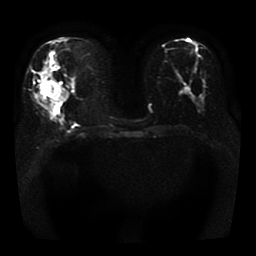
Breast MRI, one axial slice; position 18 of 41 along the scan axis; diffusion-weighted series; image 2 of 4 stored at this slice position (different b-values; order by instance number); 1.5 T; 5 mm slice thickness; 256 × 256 image matrix. Female patient.
Outlined on this slice (manually delineated by an expert):
- tumour on diffusion-weighted imaging: bounding box <39,76,58,104> (left, top, right, bottom; pixels)